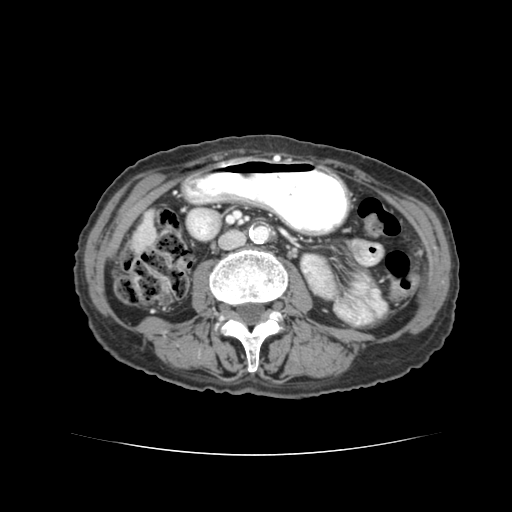
Contrast-enhanced abdominal CT (liver protocol), one axial slice. Position 7 of 77 along the scan axis. Reconstruction kernel STANDARD. Soft-tissue window (W 400 / L 40 HU). 2.5 mm slice thickness. 512 × 512 image matrix. Case-level facts recorded for this patient, not image findings: diagnosis: hepatocellular carcinoma (patient treated with transarterial chemoembolisation; whether this scan precedes or follows treatment is not stated here); TNM stage (as recorded): Stage-I; Child-Pugh class: A; tumour differentiation: well differentiated; tumour nodularity: uninodular.
Annotated regions visible in this slice (semi-automatic segmentation, software-assisted and operator-edited):
- liver parenchyma outside the tumour (the mass and vessels are separate outlines, so this box may not span the whole liver): bounding box <138,220,146,230> (left, top, right, bottom; pixels)